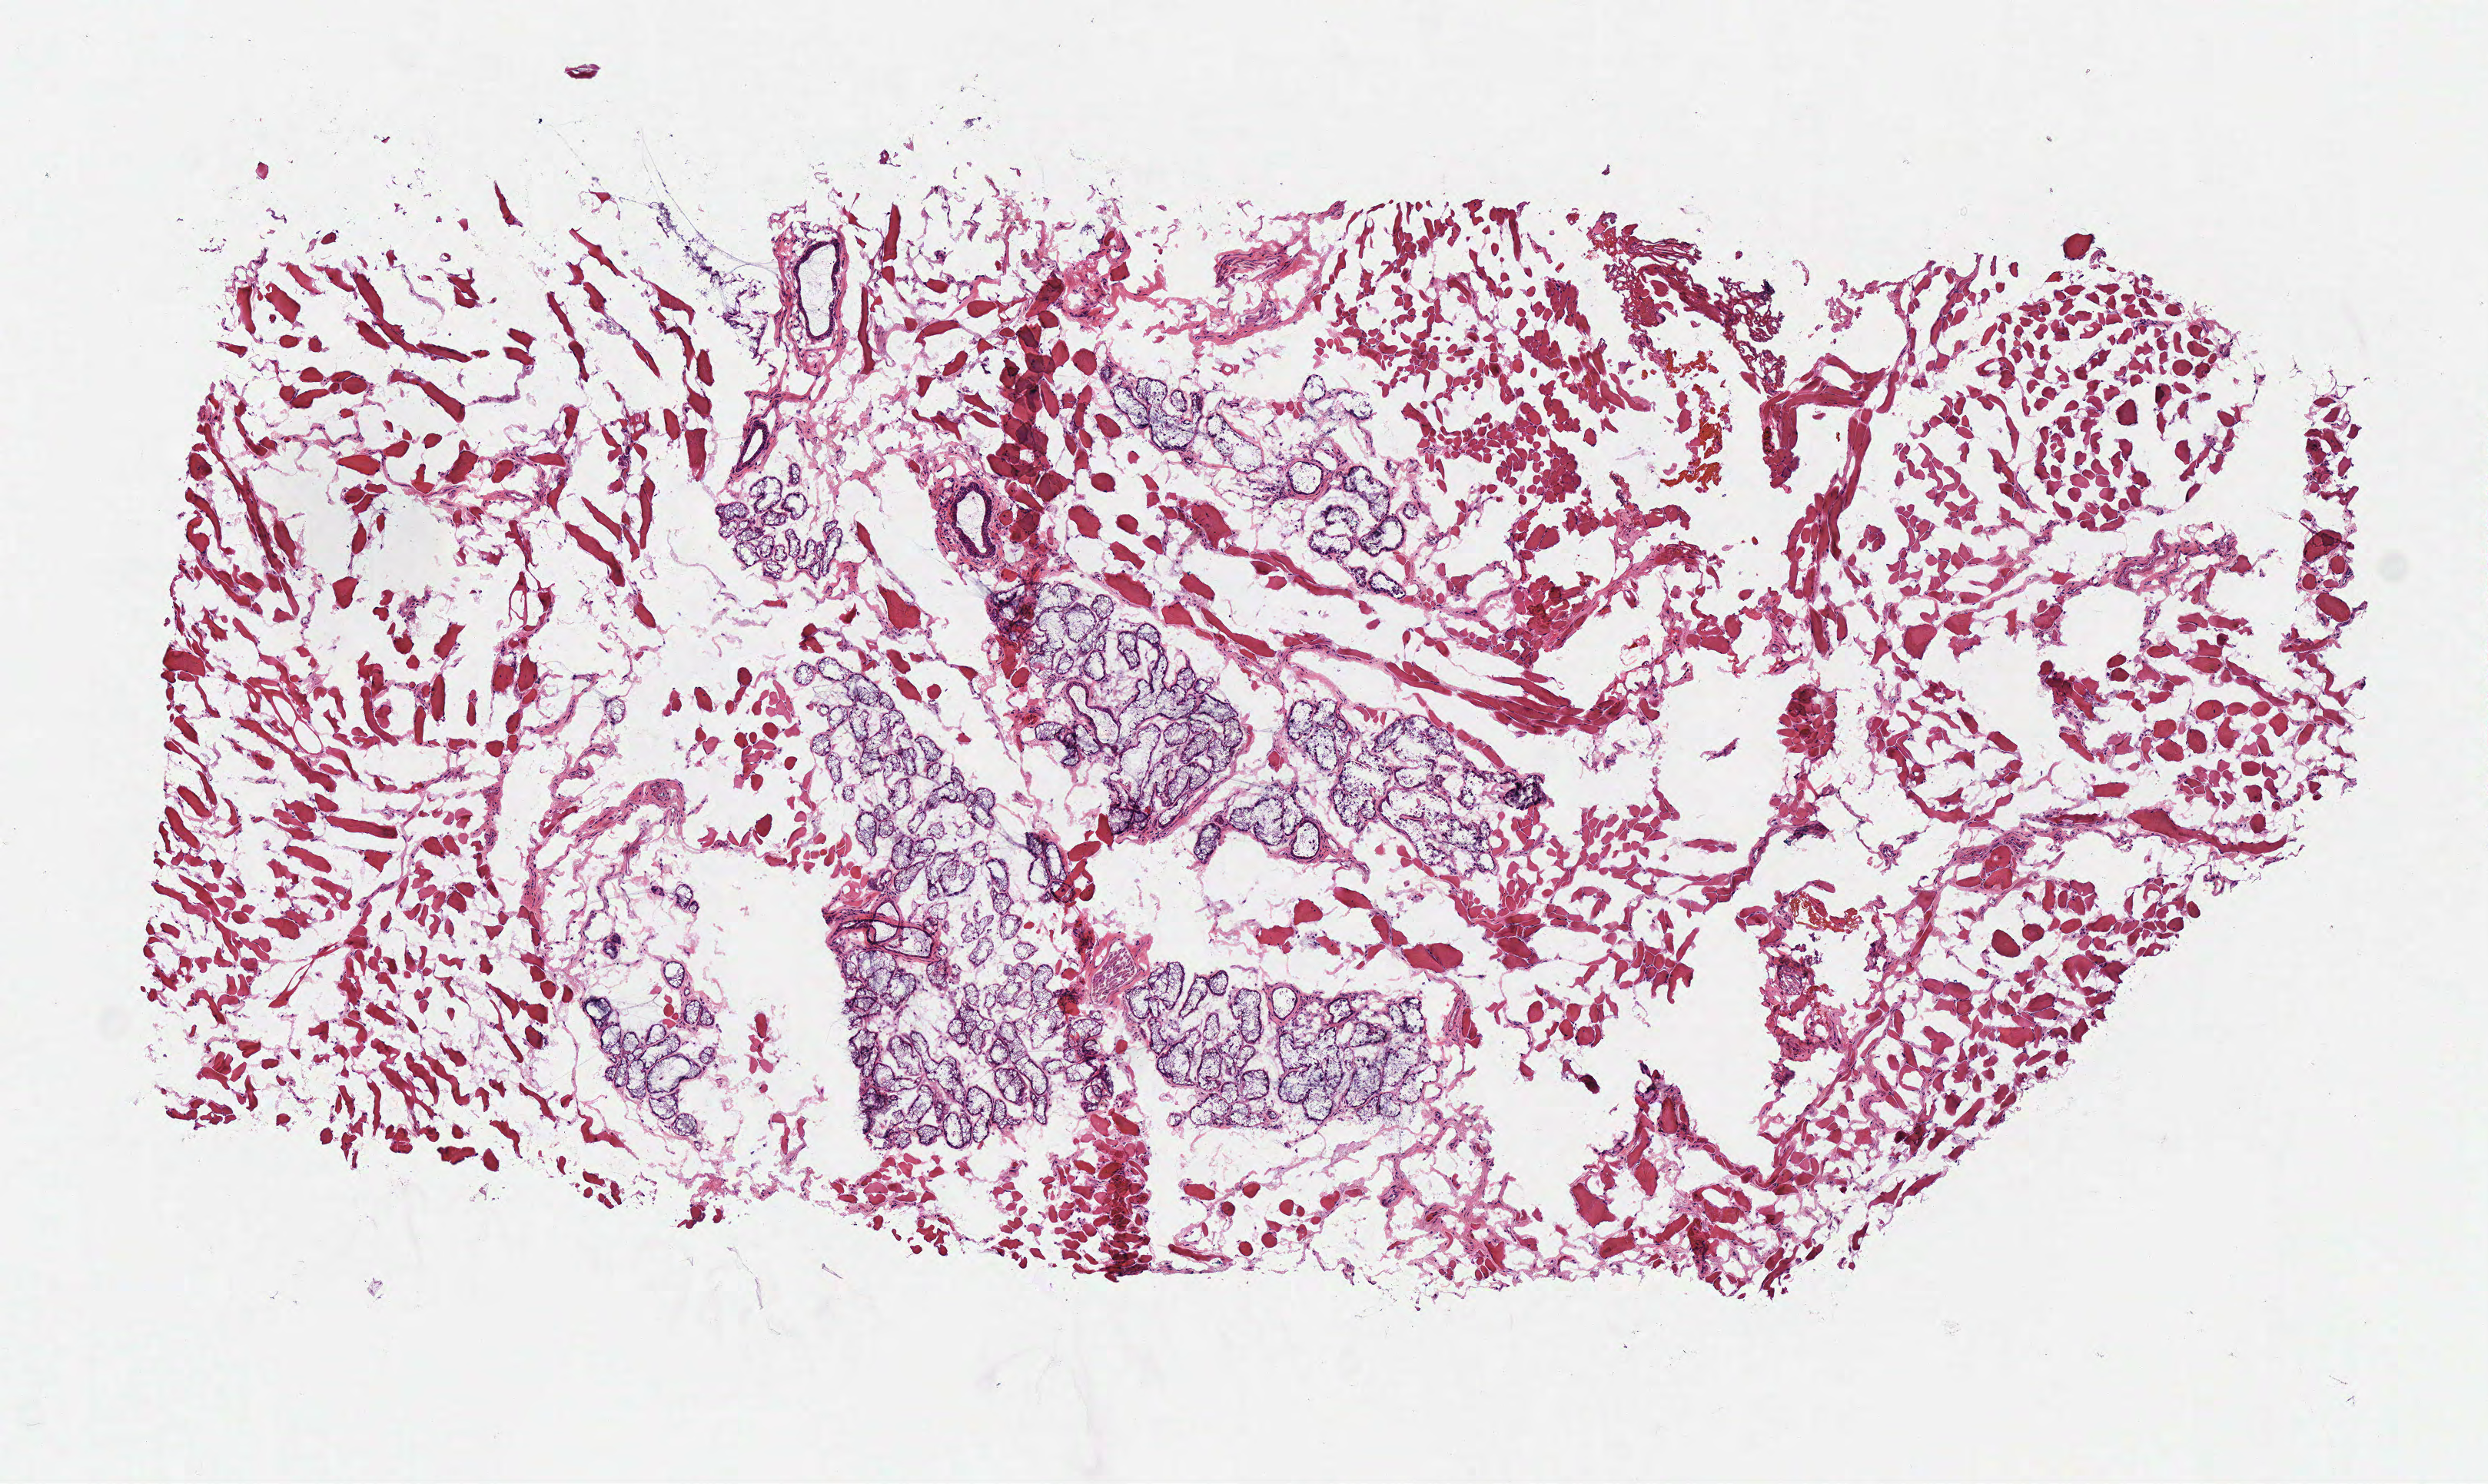
H&E-stained whole-slide image, low-resolution overview of the scanned area, about 6.4 x 3.8 mm (from a 40x scan); frozen section from the top of the tissue portion; solid tissue normal (non-tumour tissue) sample from the head and neck. Male patient; age at initial diagnosis 54 years.
This section: solid tissue normal (non-tumour) sample from the same patient. Patient diagnosis: Squamous cell carcinoma, NOS.